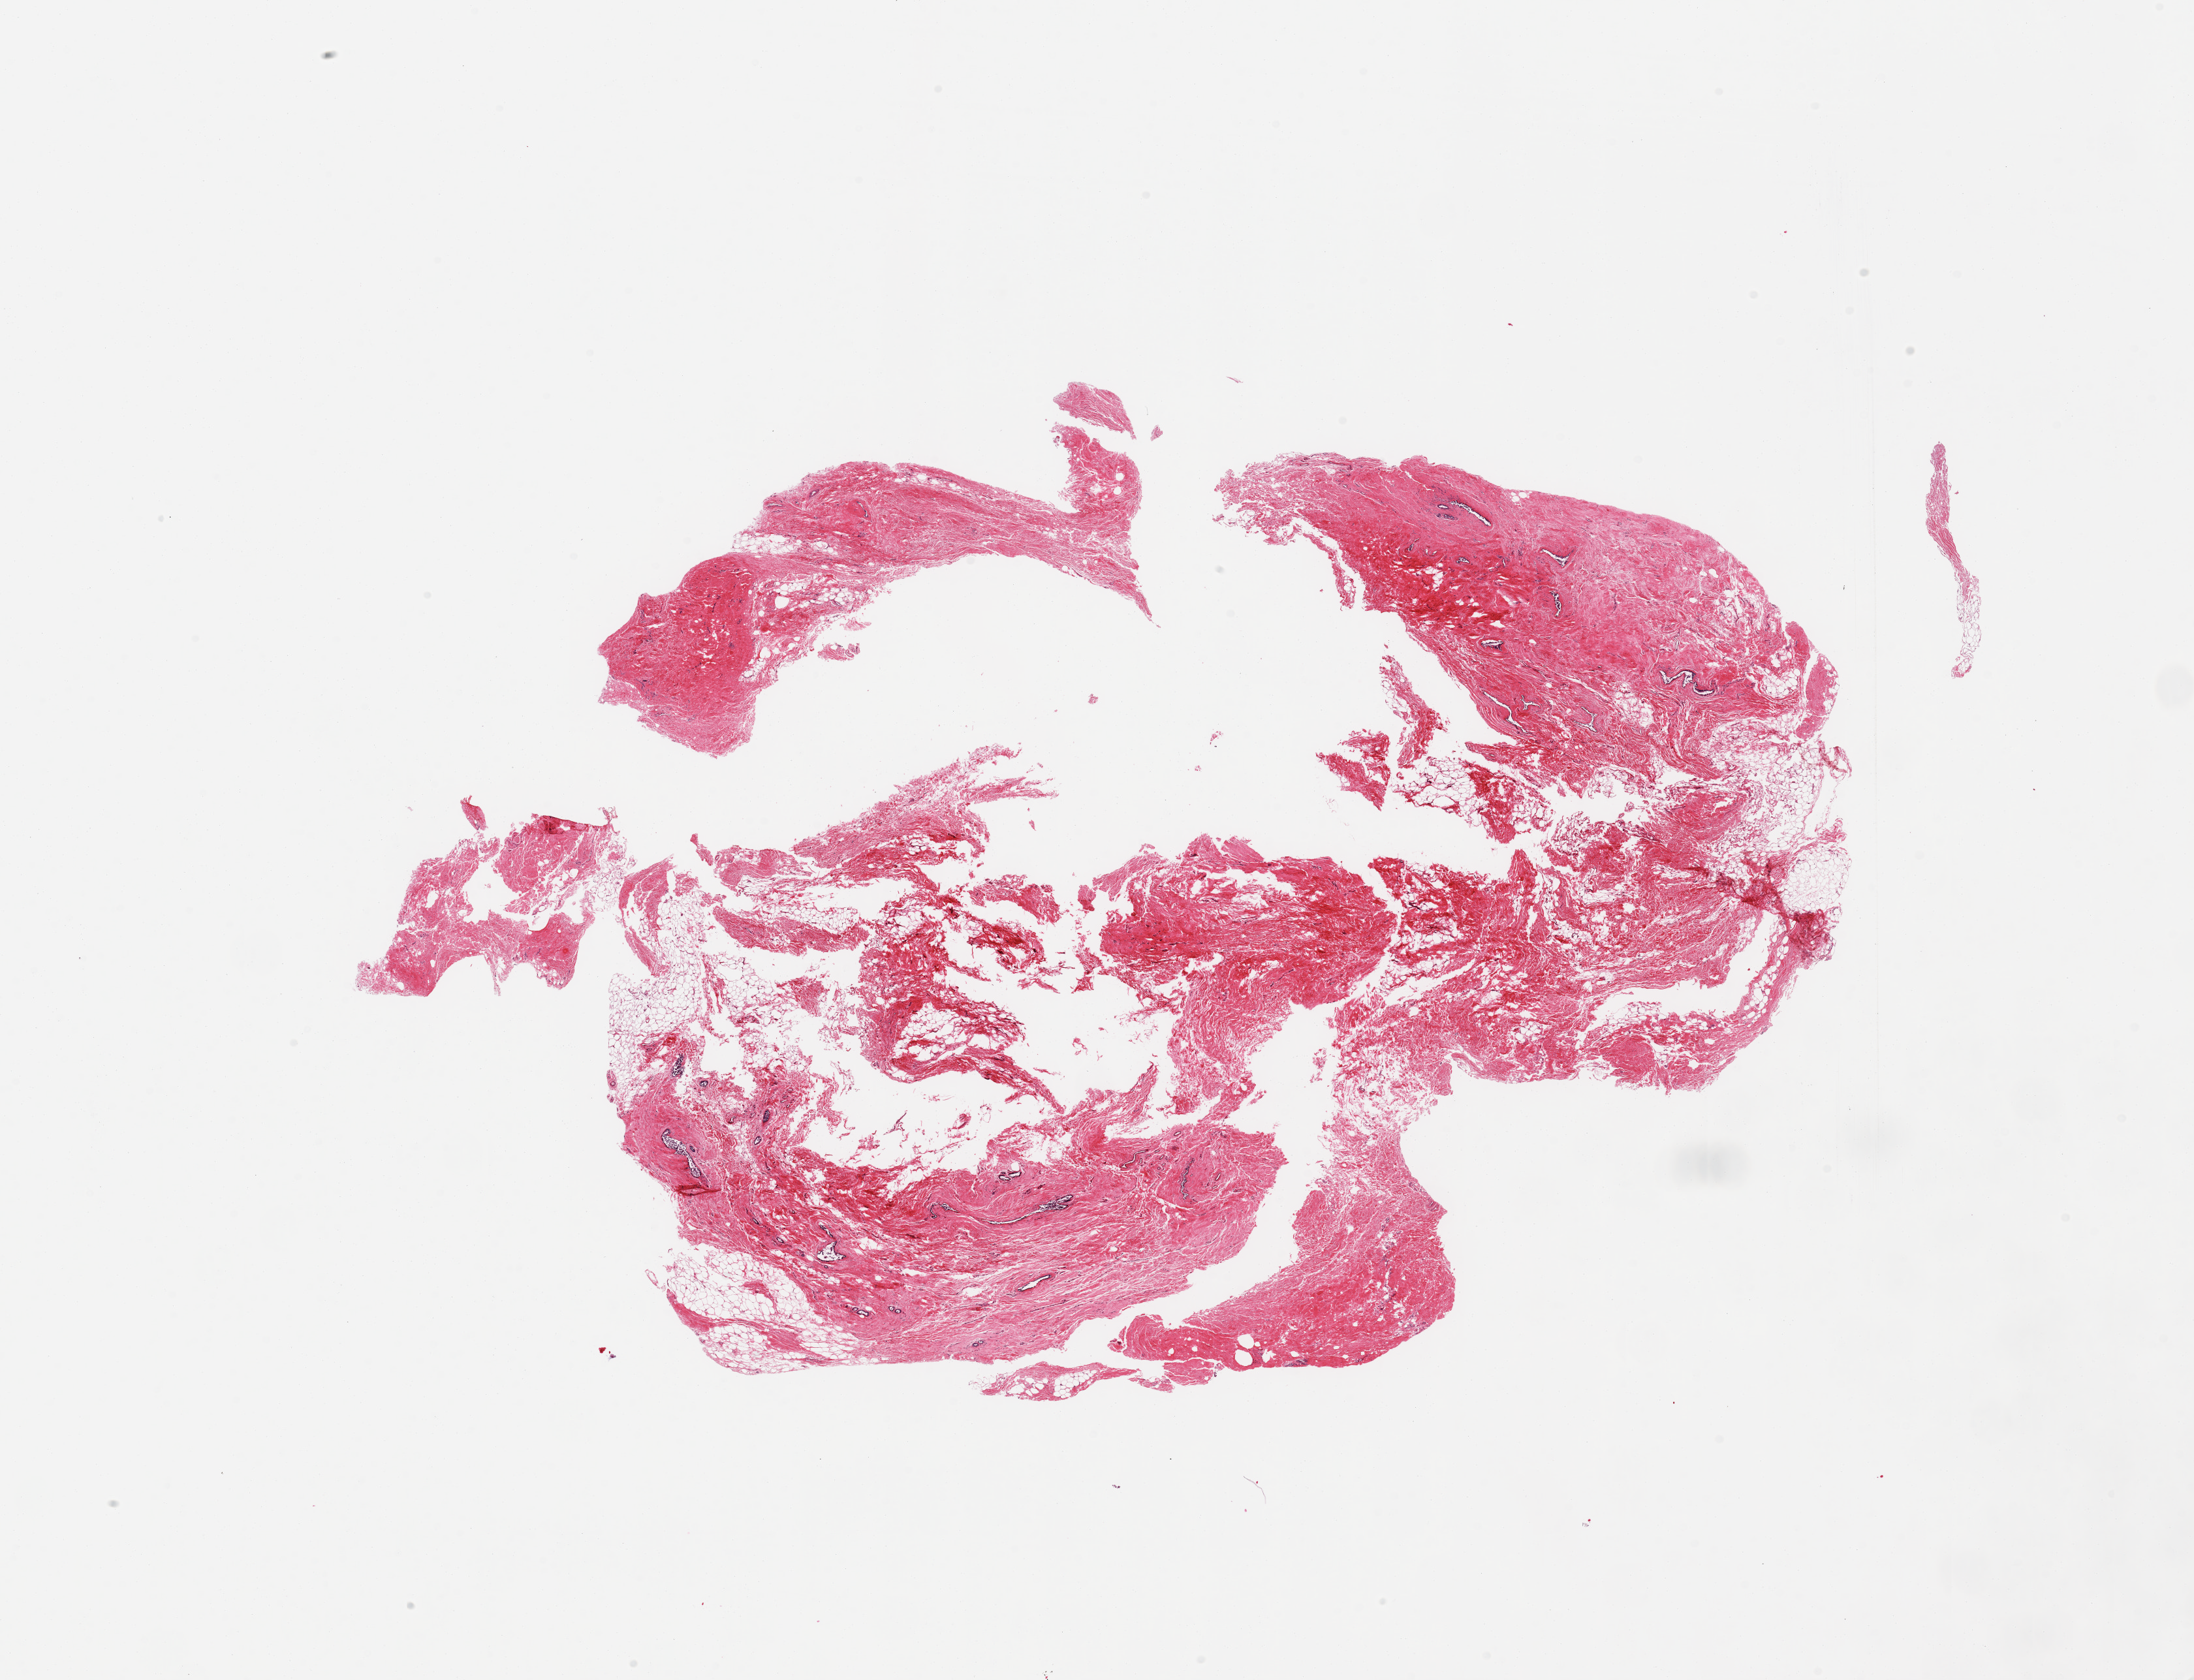
Hematoxylin and eosin (H&E) whole-slide image, brightfield — low-resolution overview of the scanned area, about 26.6 x 20.4 mm (slide scanned at 20x). PAXgene-fixed, paraffin-embedded tissue. Sampled site (target tissue): breast. Donor tissue sample.
Pathologist's review note for this sample: 1 piece (fragments), gynecomastoid stromal and ductal hyperplasia-ductal elements poorly preserved.